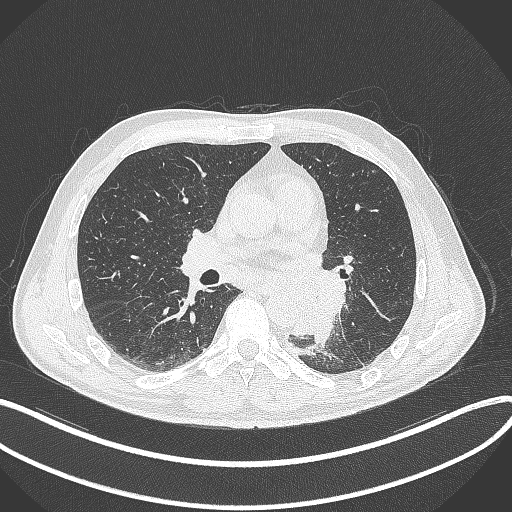
Chest CT, one axial slice; position 174 of 329 along the scan axis; 120 kVp; lung window (W 1500 / L -600 HU); 1 mm slice thickness; 512 × 512 image matrix. Patient: male, 59 years. Case-level facts recorded for this patient, not image findings: clinical TNM (as recorded): T2a N2 M0.
Structures marked on this image (rectangle marked by the reading radiologist):
- lung tumour (recorded histology: squamous cell carcinoma): box from (x=269, y=263) to (x=349, y=341) px